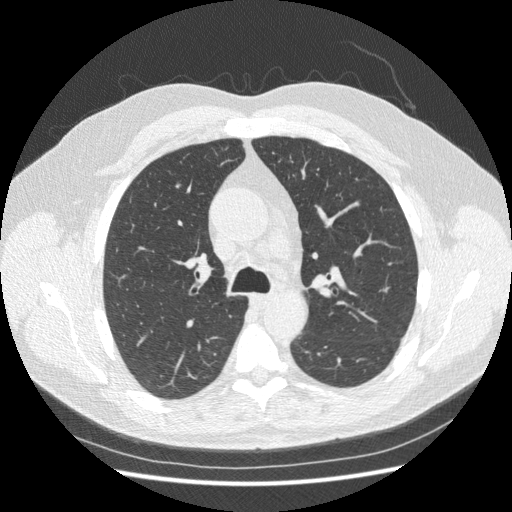
Low-dose screening chest CT, axial slice, first (baseline) screen, lung window (W 1500 / L -600 HU), 120 kVp, slice 90 of 250 in the series, 512 × 512 image matrix. Male participant, aged 63 years at enrolment. Current smoker at enrolment.
Expert reader's lesion annotation, bounding box <168,177,186,195> (left, top, right, bottom; pixels). Reader record for this screening exam (exam-level; its link to the box is not recorded): non-calcified nodule or mass ≥4 mm, right upper lobe, 5 × 4 mm, smooth margins, soft tissue attenuation. Official screen result: positive, change unspecified: nodule(s) >= 4 mm or enlarging nodule(s), mass(es), or other non-specific abnormalities suspicious for lung cancer.